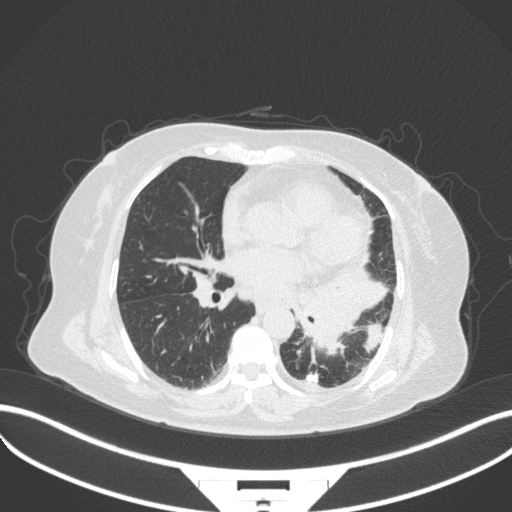
Chest CT, one axial slice; slice 165 of 328 in the series (ordered by position); lung window (W 1500 / L -600 HU); 1 mm slice thickness; 512 × 512 image matrix, field of view 400 × 400 mm. Female patient, age 69 years. Case-level facts recorded for this patient, not image findings: clinical TNM (as recorded): T2b N3 M1.
Annotated regions visible in this slice (rectangle marked by the reading radiologist):
- lung tumour (recorded histology: adenocarcinoma): box from (x=297, y=262) to (x=389, y=357) px